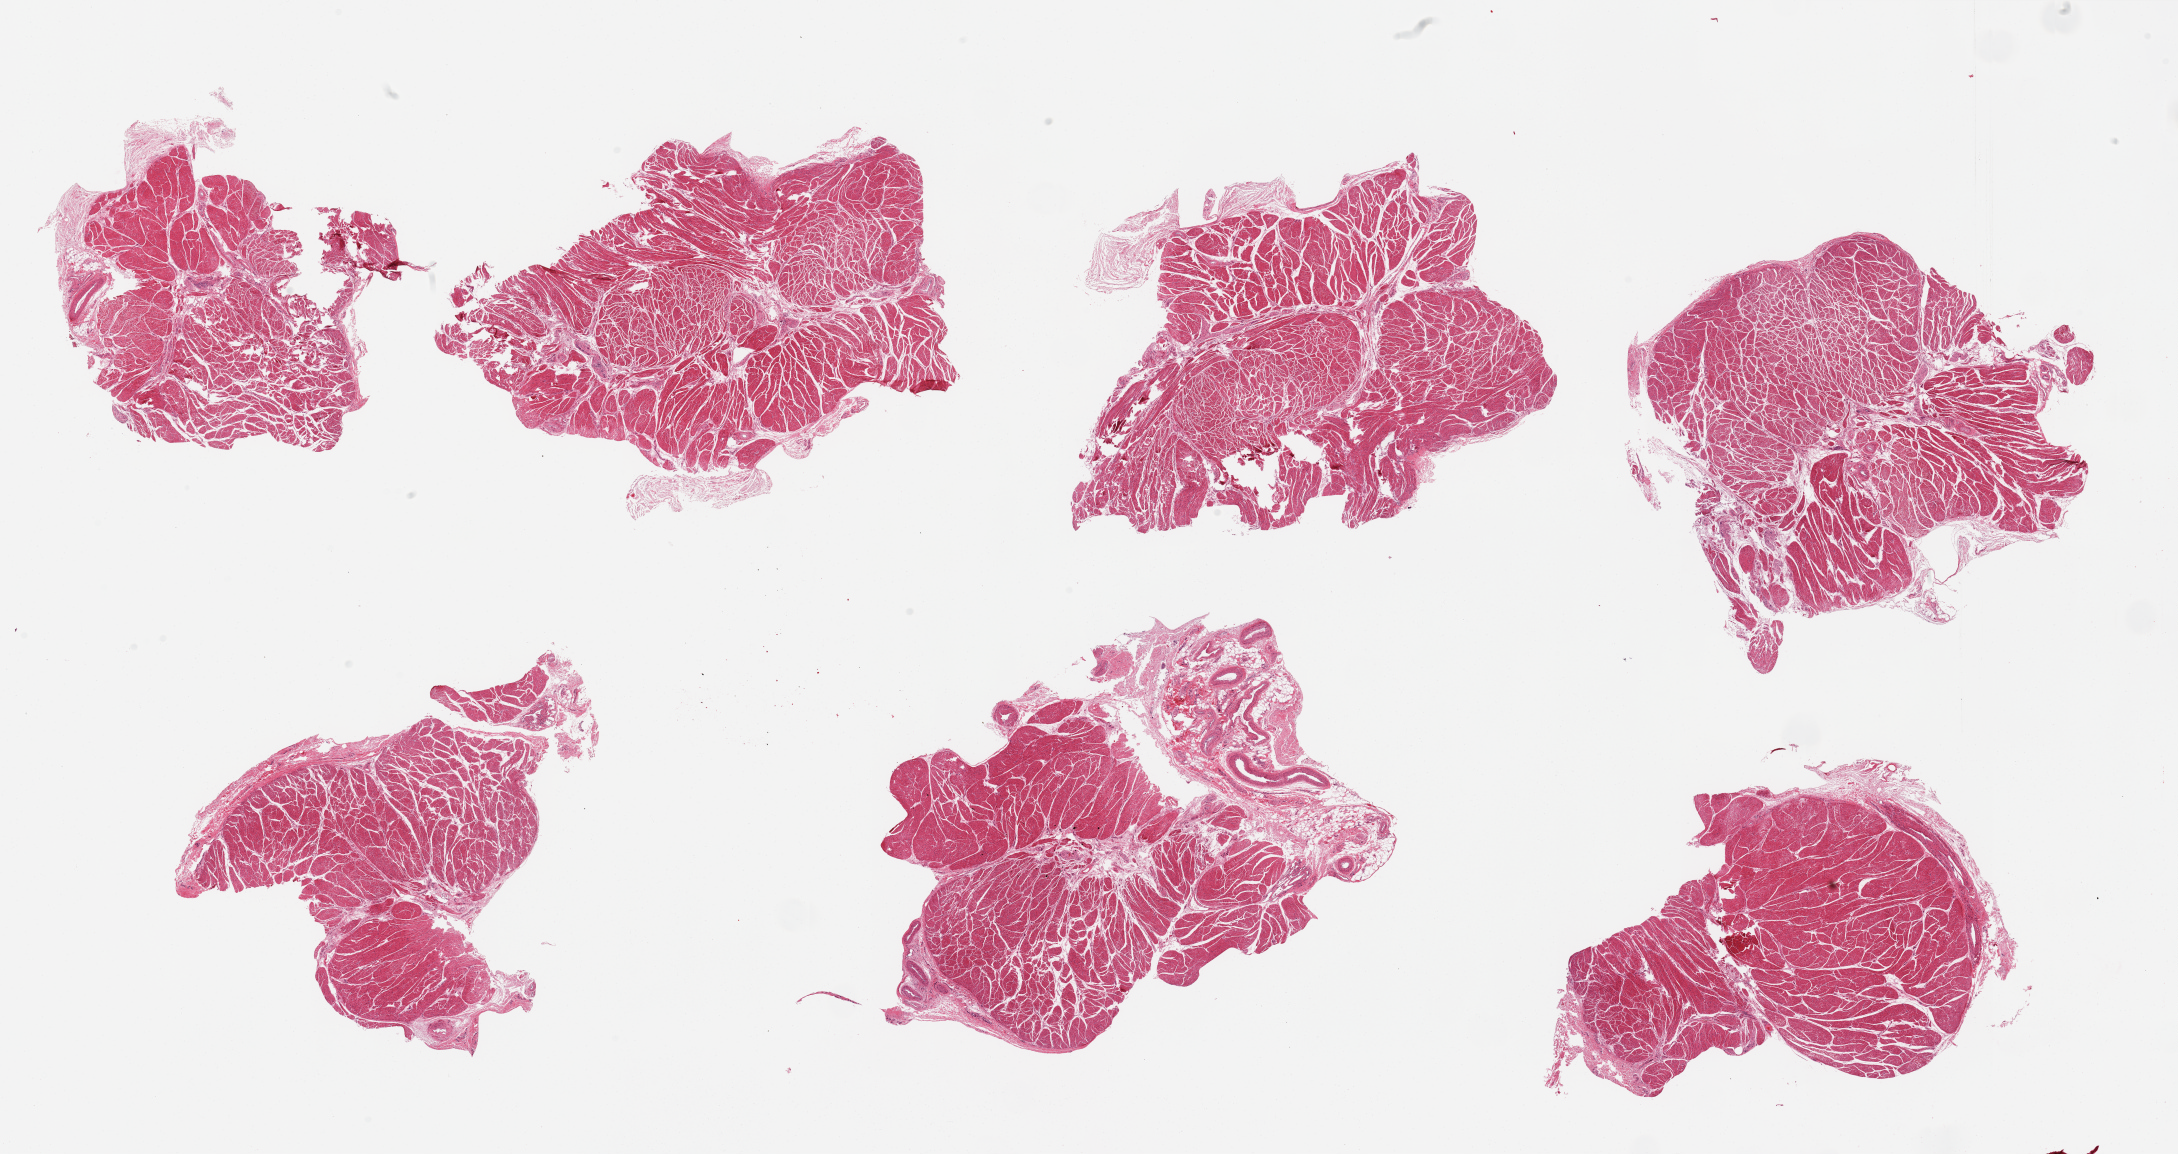
H&E whole-slide image, whole scanned area (about 34.5 x 18.3 mm) shown as a low-resolution overview, PAXgene-fixed, paraffin-embedded tissue, section of esophageal muscle (target tissue), donor tissue sample. Male donor.
Pathologist's review note for this sample: 7 pieces, all muscularis, adherent nubbin serosa in one section.